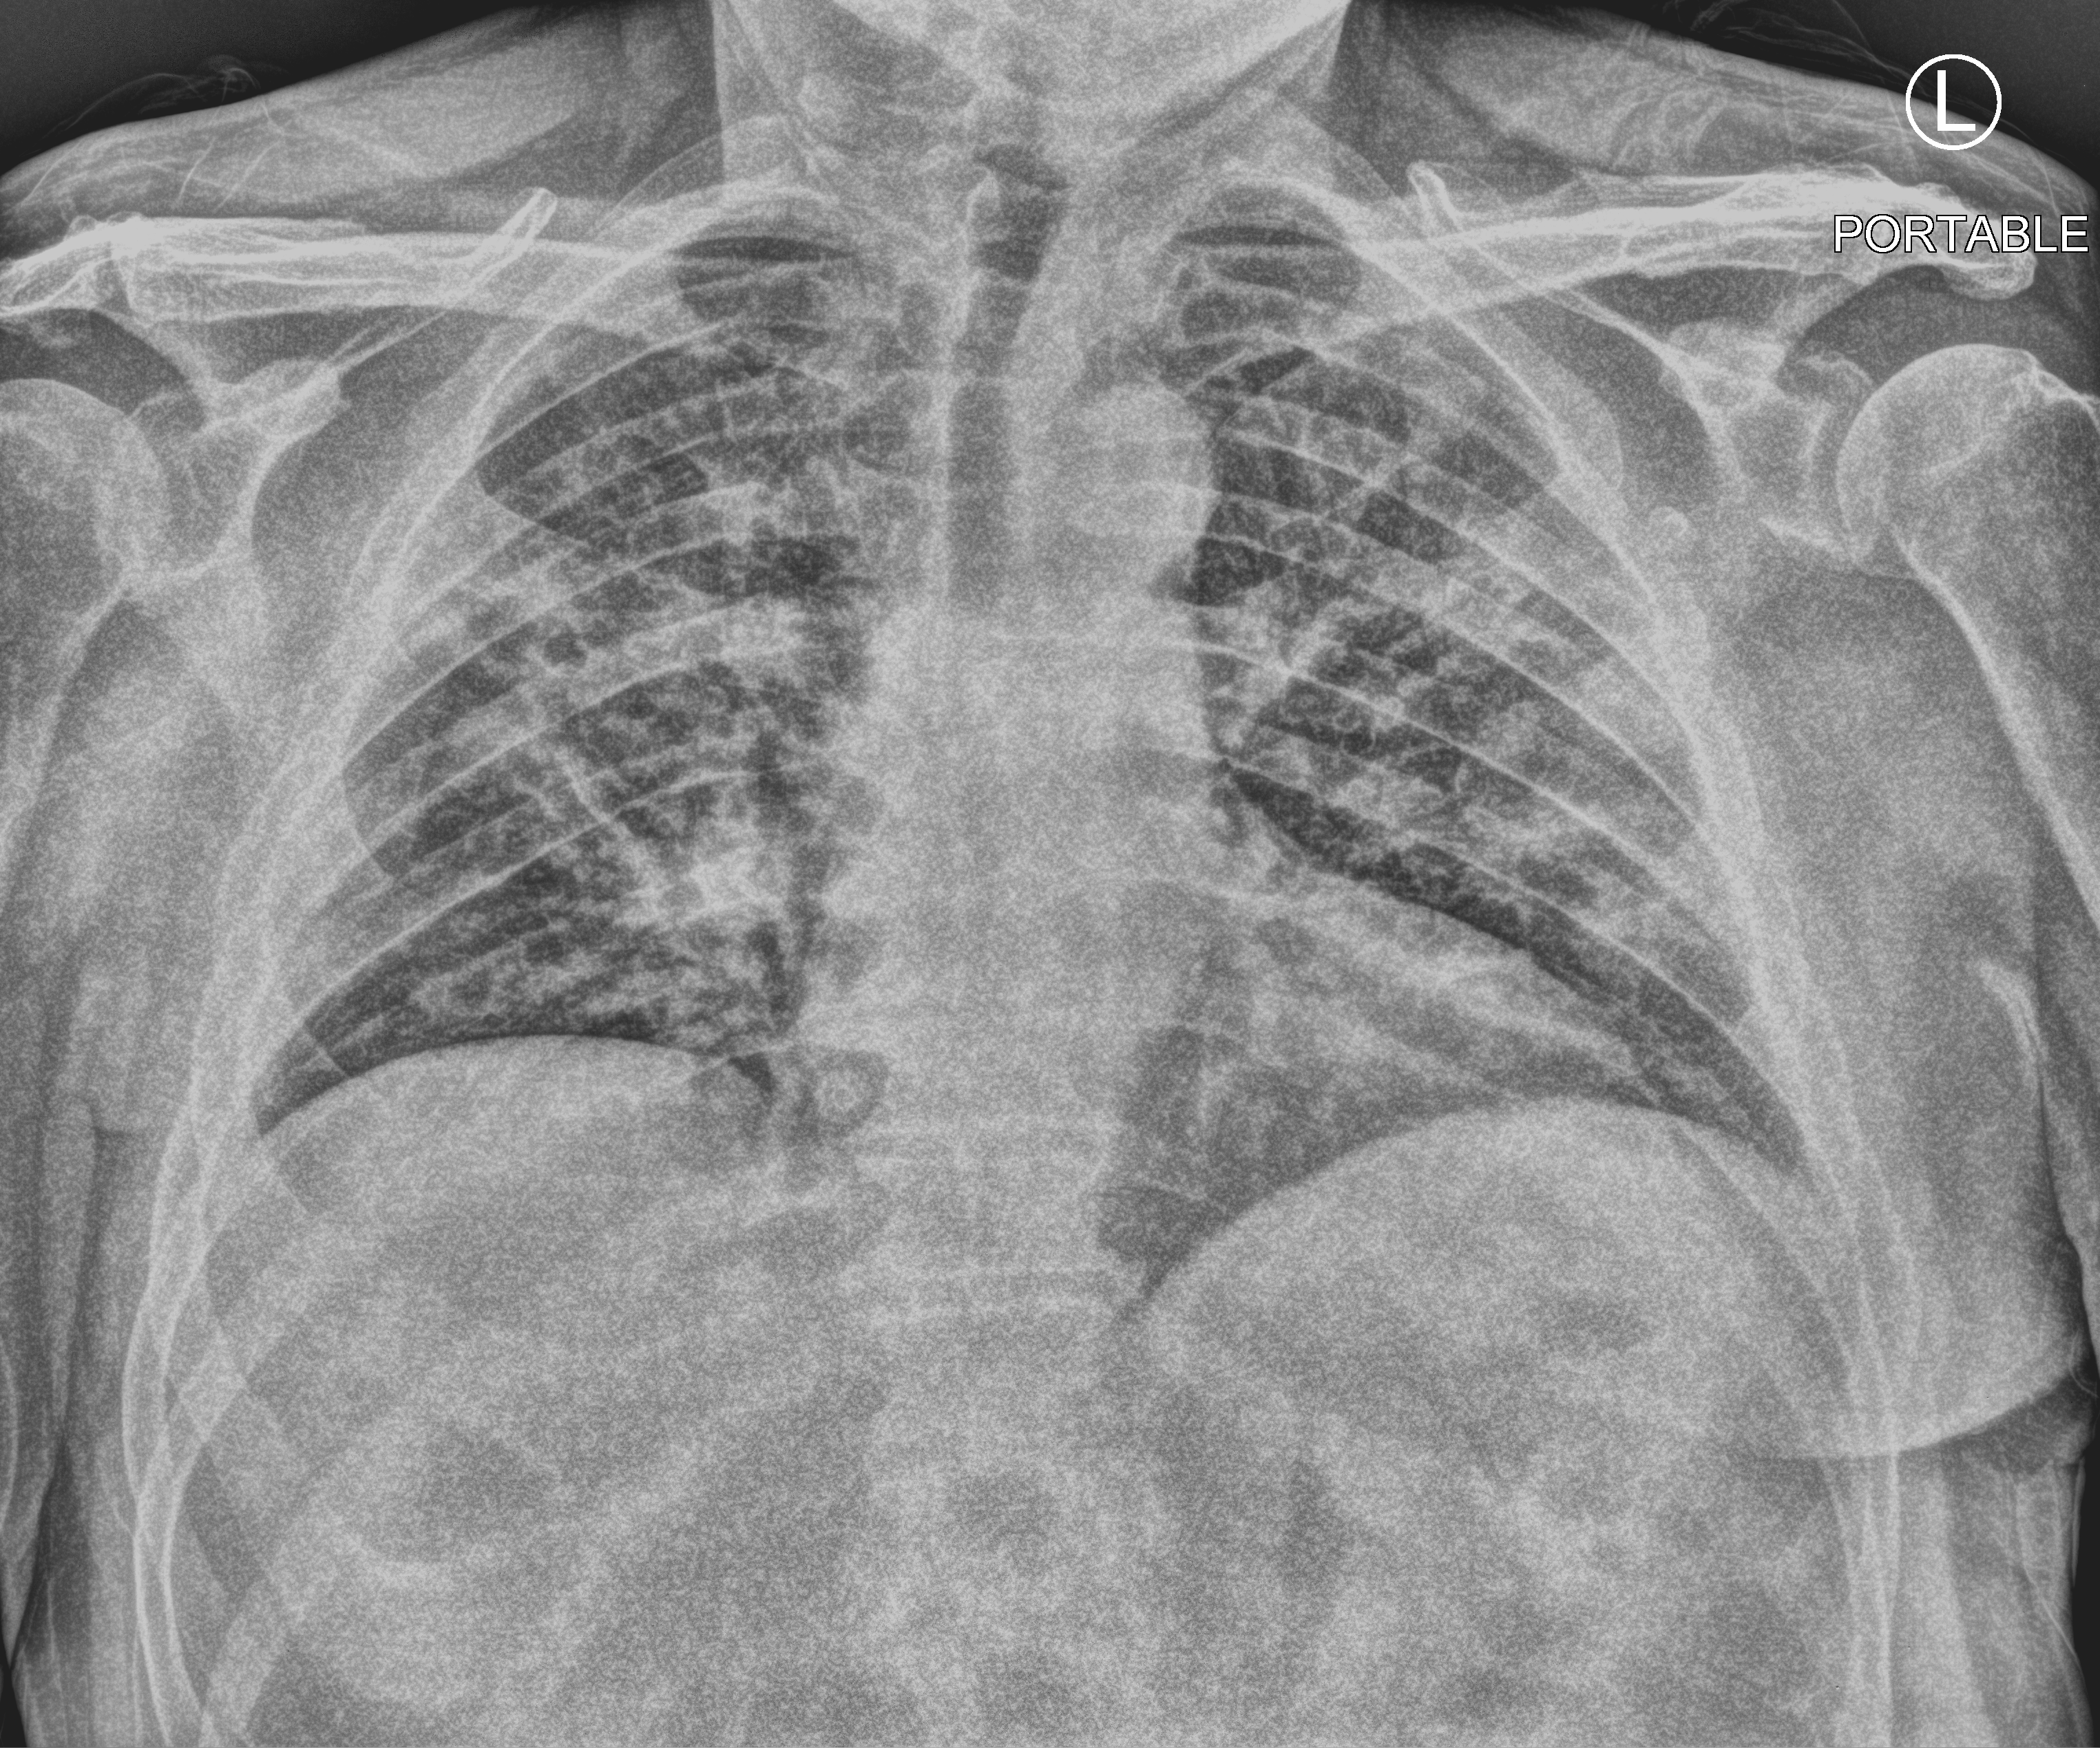
Bedside chest radiograph (computed radiography); anteroposterior (AP) projection. Male patient hospitalised with COVID-19, age 60–74 years.
Admission-level facts for this patient (not findings on this image; timing relative to this image not recorded):
- mechanically ventilated during this hospital stay: no
- length of hospital stay: 16 days
- diabetes (admission record): yes